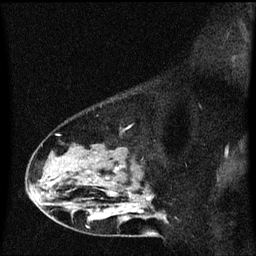
Breast MRI (dynamic contrast-enhanced), one sagittal slice; slice 41 of 60 in the series (ordered by position); dynamic contrast-enhanced series, image 2 of 3 at this slice position (ordered by acquisition); 1.5 T; TE 4.2 ms, TR 8.4 ms; 2 mm slice thickness; 256 × 256 image matrix, field of view 200 × 200 mm. Female patient, age 49 years. Case-level facts recorded for this patient, not image findings: setting: breast cancer imaged before/during neoadjuvant chemotherapy; receptor status: HR-positive, HER2-negative.
Structures marked on this image (semi-automatic segmentation, software-assisted and operator-edited):
- analysis volume of interest (the breast-tissue region the enhancement analysis was run in; not a lesion): box from (x=27, y=106) to (x=168, y=221) px
- tumour enhancement mask (voxels above the 70 % enhancement threshold inside the analysis volume of interest): (x=140, y=198)–(x=152, y=213)